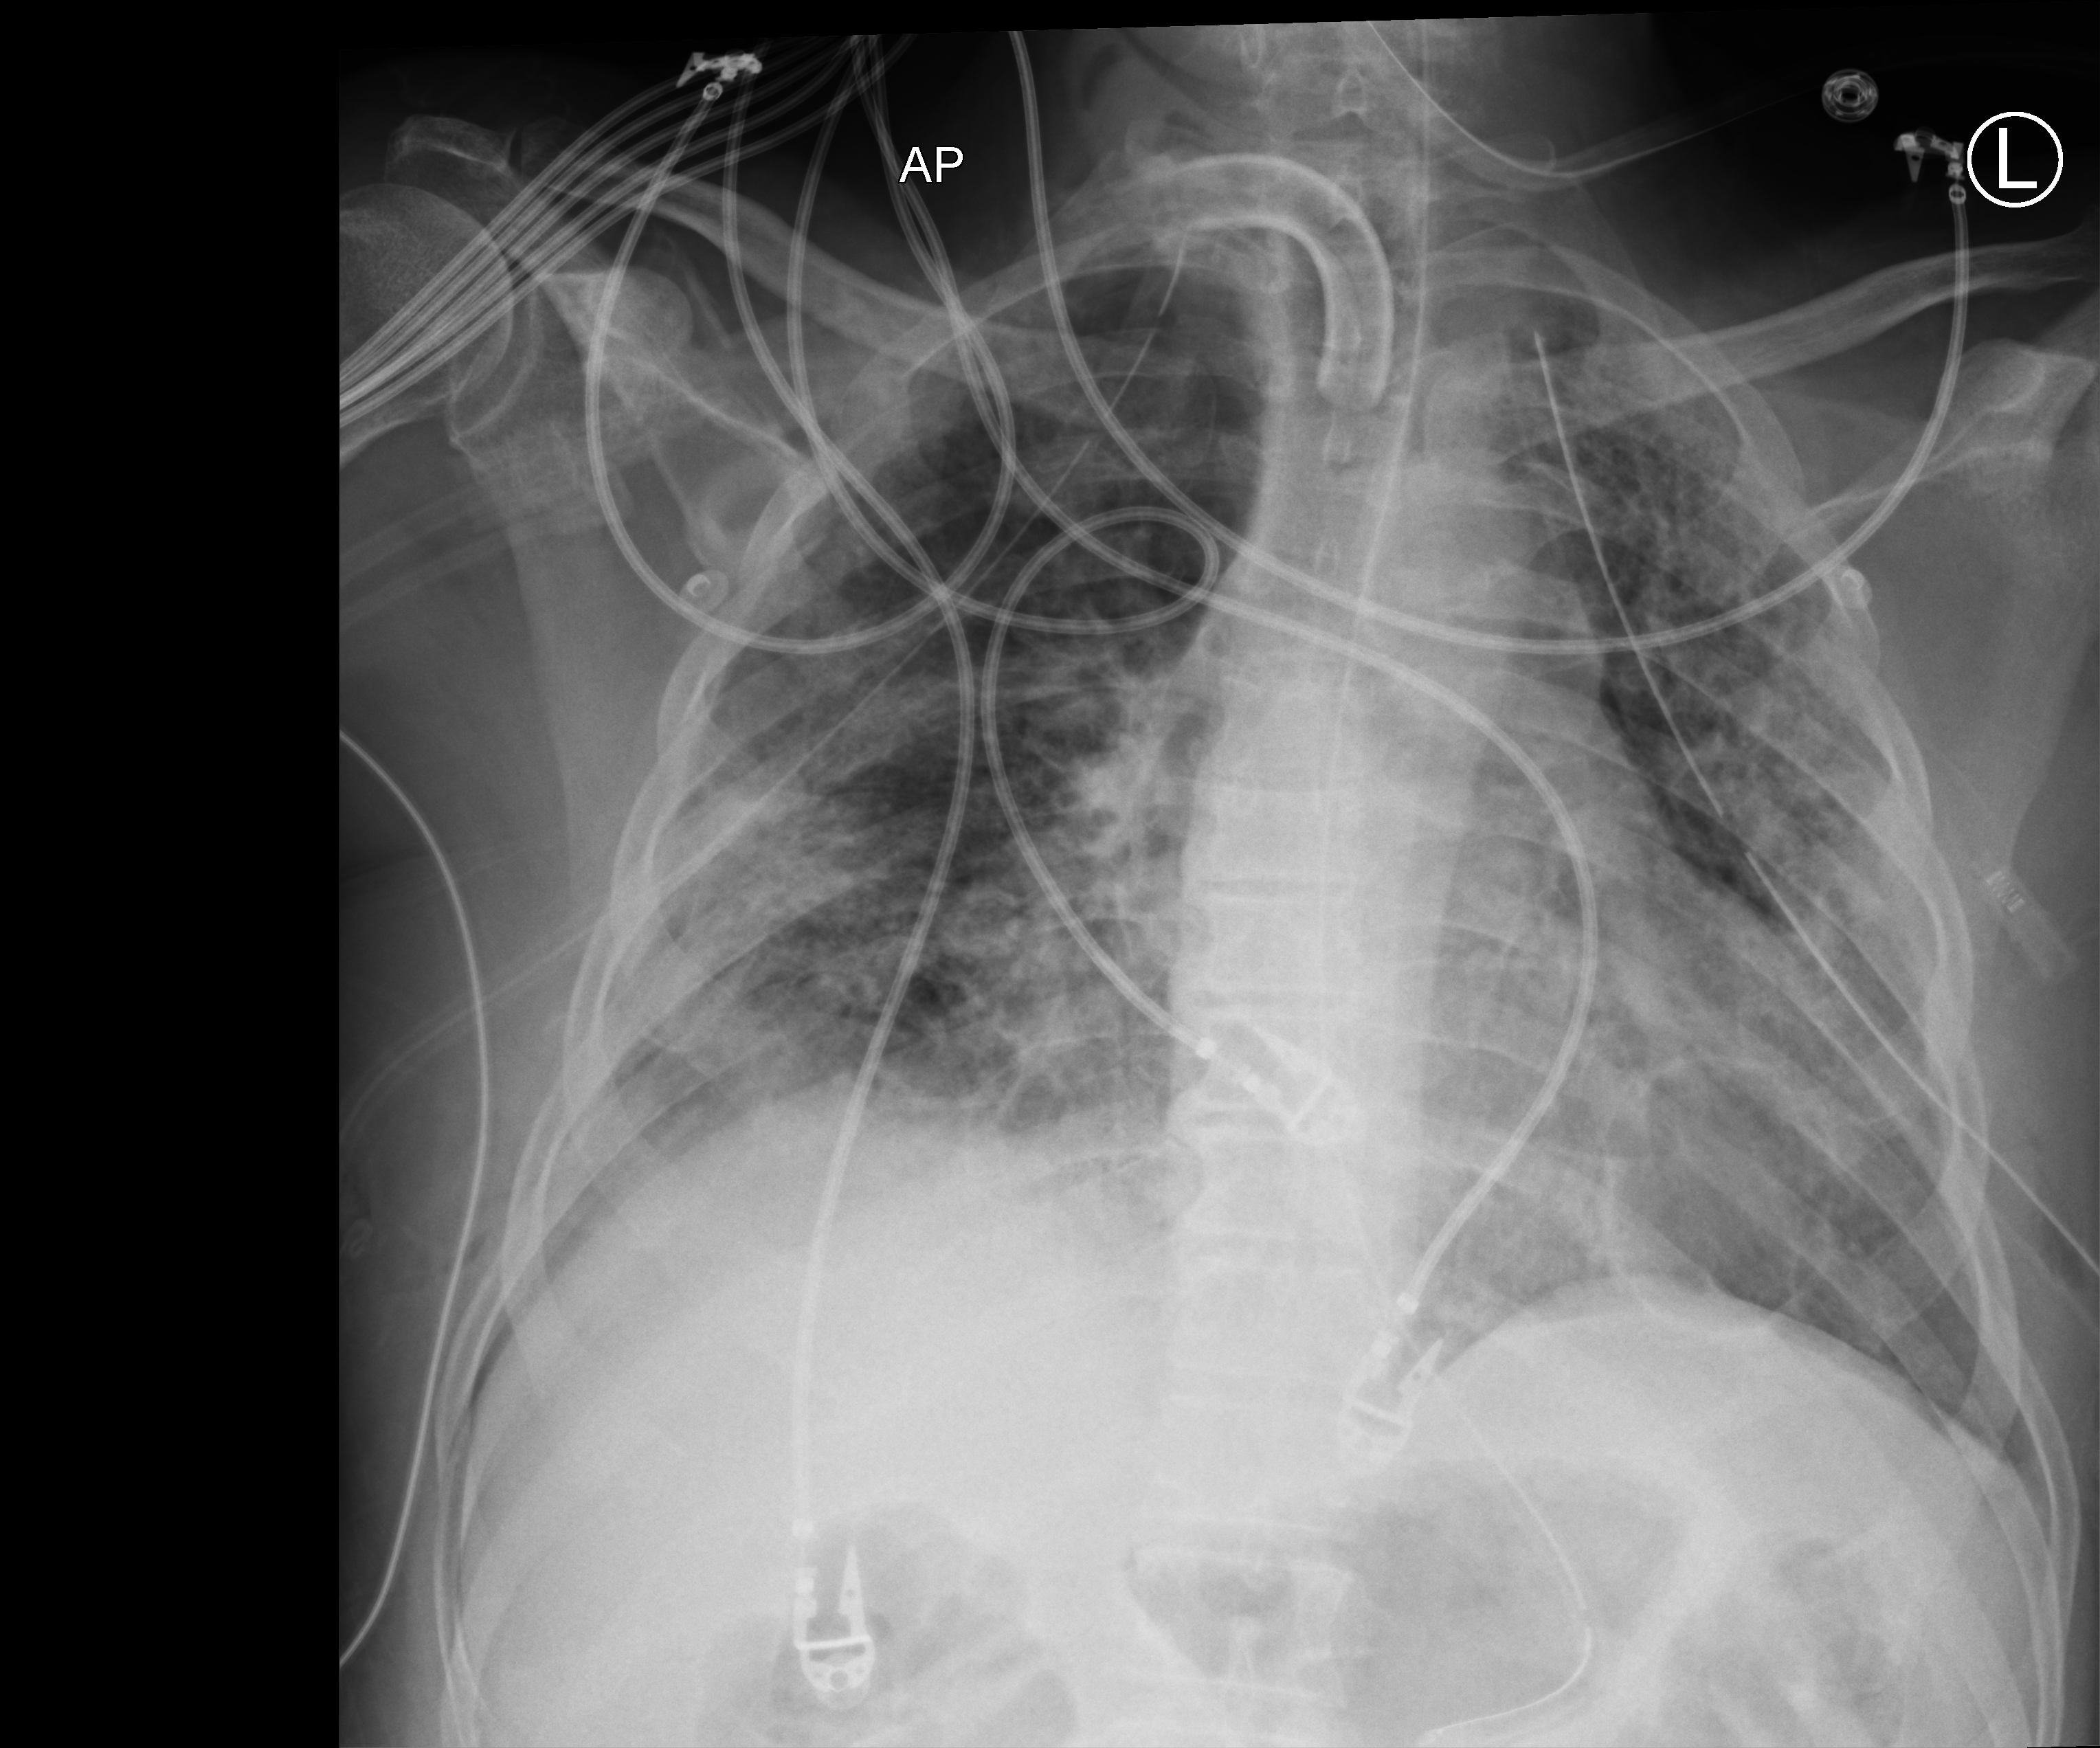
Chest X-ray (portable), anteroposterior (AP) projection. Patient hospitalised with COVID-19; male, aged 18–59 years.
Admission-level facts for this patient (not findings on this image; timing relative to this image not recorded):
- COPD (admission record): no